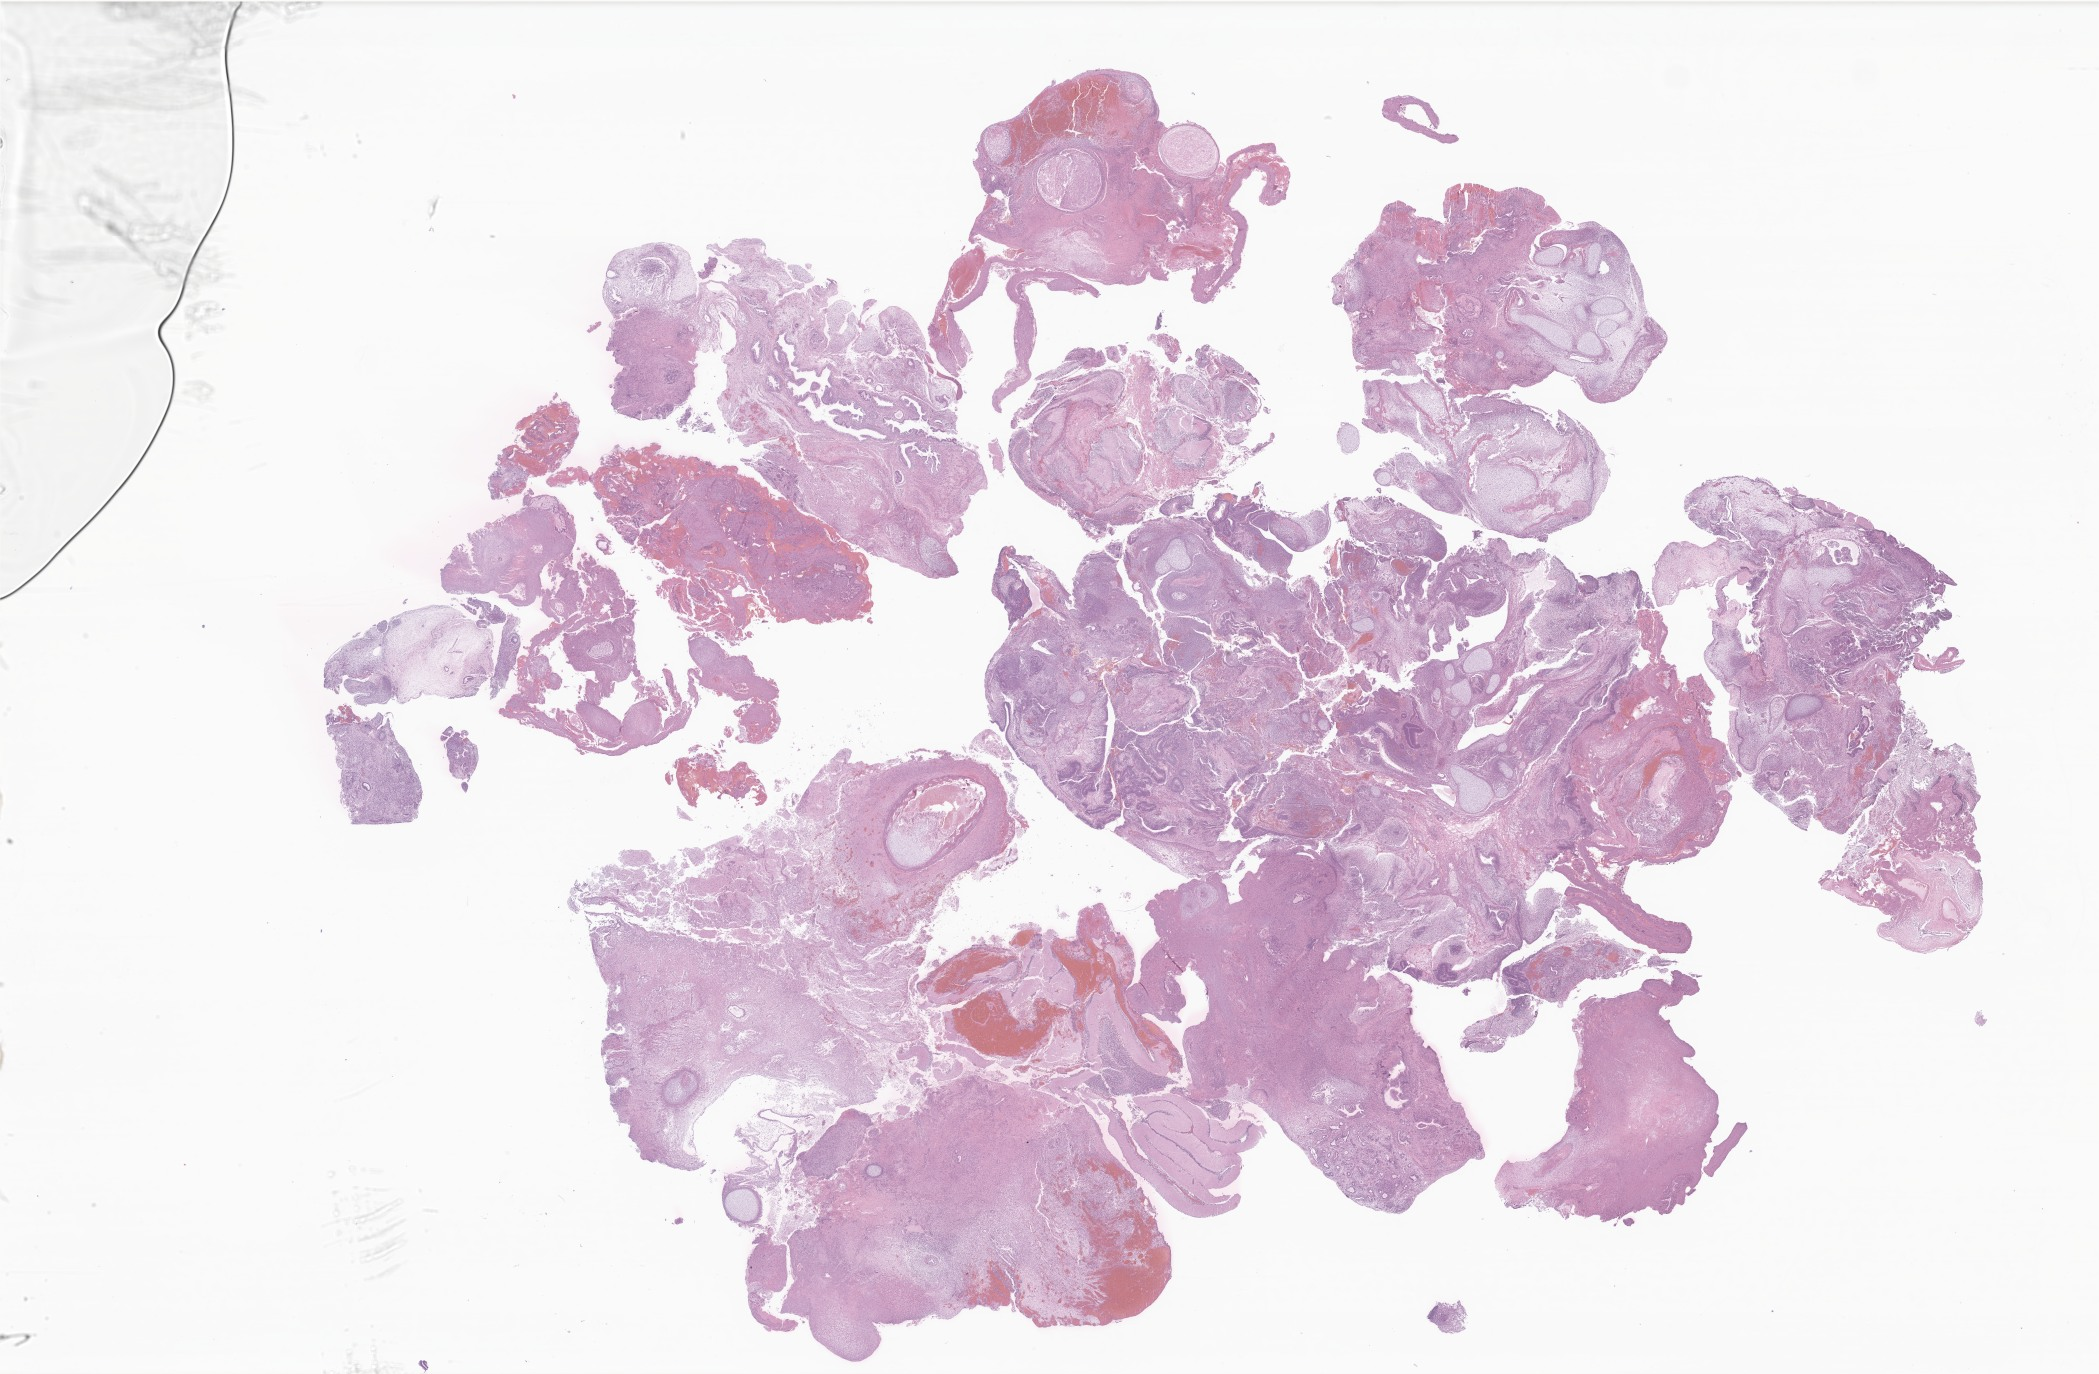
Haematoxylin and eosin whole-slide image of tumor tissue from the brain — a low-resolution overview of the entire scanned area, about 35.4 x 23.2 mm. FFPE section. Patient: female, age 83 days.
• recorded diagnosis: Teratoma, NOS